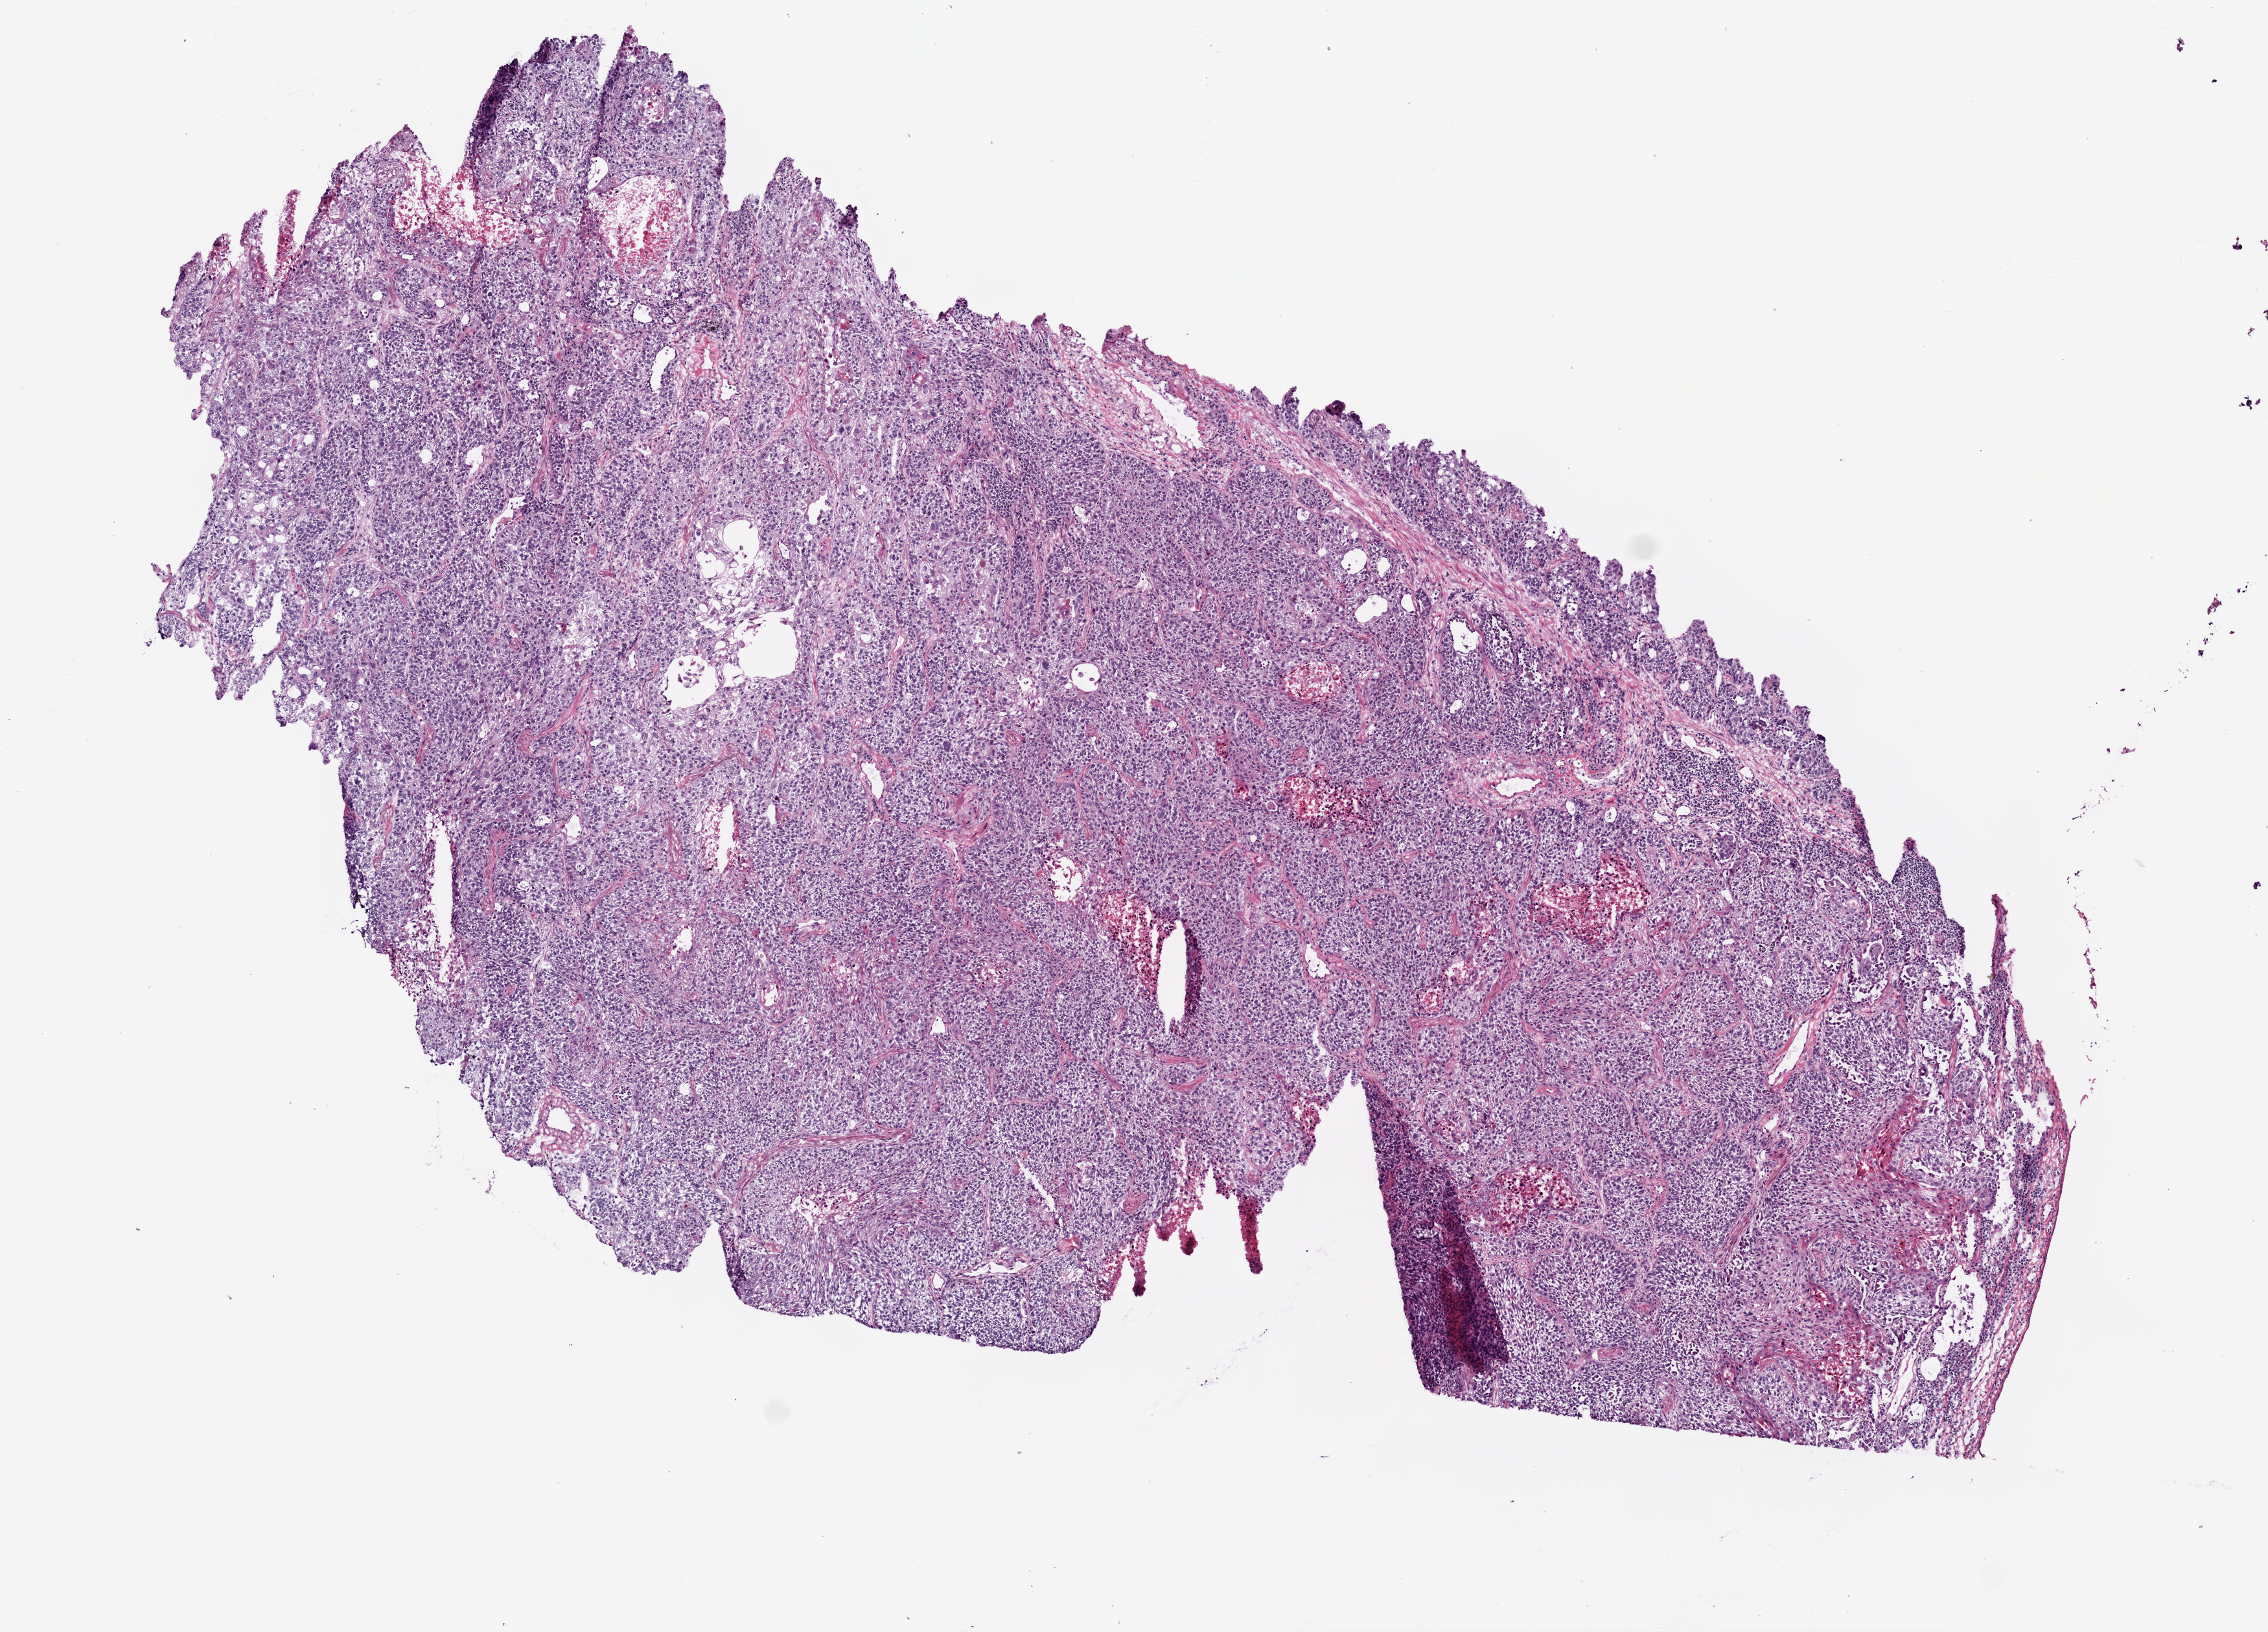
Digitized H&E tissue section (whole slide), shown as a low-resolution overview of the whole scanned area (about 7.0 x 5.1 mm); frozen section from the bottom of the tissue portion; lung, primary tumour sample. Female patient; age at initial diagnosis 73 years. Composition of this section per pathologist review: tumour cells 87%, tumour nuclei 85%, normal cells 3%, stromal cells 5%, necrosis 5%.
Diagnosis: Squamous cell carcinoma, NOS (upper lobe, lung). AJCC pathologic stage: IIIA. Laterality: right.